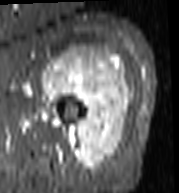
MRI of an extremity soft-tissue mass, one axial slice; slice 77 of 103 in the series (ordered by position); STIR; MR volume resampled by the dataset authors to the PET/CT grid (not the native acquisition matrix); 3.27 mm slice thickness; 179 × 193 image matrix, field of view 175 × 188 mm. Female patient. From the clinical record (not read from this slice): histological type: undifferentiated – high grade; grade: high; site of the primary tumour: left thigh.
Annotated regions visible in this slice (expert contour drawn on MRI and transferred to this co-registered scan by the dataset authors):
- gross tumour volume including surrounding oedema: bounding box (x1, y1, x2, y2) in pixels: (41, 46, 131, 170)
- gross tumour volume (mass): (43, 46, 131, 170)